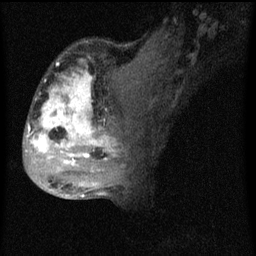
Breast MRI (dynamic contrast-enhanced), one sagittal slice; position 29 of 60 along the scan axis; dynamic contrast-enhanced series, image 2 of 4 at this slice position (ordered by acquisition); 1.5 T; TE 4.2 ms, TR 8 ms; 2 mm slice thickness; 256 × 256 image matrix, field of view 180 × 180 mm. Patient: female, 50 years.
Annotated regions visible in this slice (semi-automatically segmented with operator editing):
- analysis volume of interest (the breast-tissue region the enhancement analysis was run in; not a lesion): box from (x=26, y=44) to (x=124, y=177) px
- tumour enhancement mask (voxels above the 70 % enhancement threshold inside the analysis volume of interest): (x=26, y=60)–(x=119, y=165)